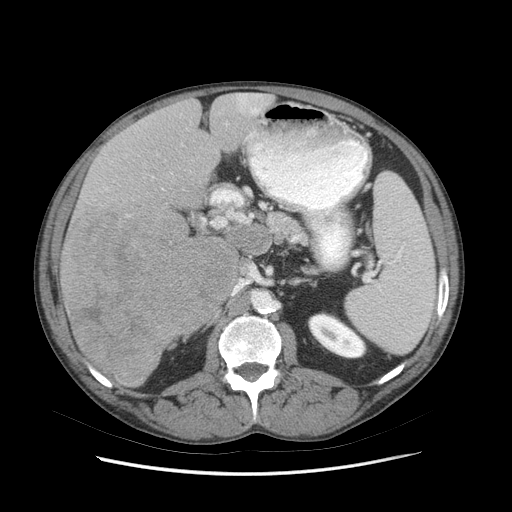
Contrast-enhanced abdominal CT (liver protocol), one axial slice; position 39 of 89 along the scan axis; reconstruction kernel STANDARD; 140 kVp; soft-tissue window (W 400 / L 40 HU); 512 × 512 image matrix. From the clinical record (not read from this slice): diagnosis: hepatocellular carcinoma (patient treated with transarterial chemoembolisation; whether this scan precedes or follows treatment is not stated here); TNM stage (as recorded): Stage-IIIB; Child-Pugh class: A; tumour nodularity: multinodular.
Structures marked on this image (semi-automatically segmented with operator editing):
- liver parenchyma outside the tumour (the mass and vessels are separate outlines, so this box may not span the whole liver): bounding box <60,92,274,388> (left, top, right, bottom; pixels)
- mass: <59,203,236,384>
- liver vessels: <229,94,262,215>